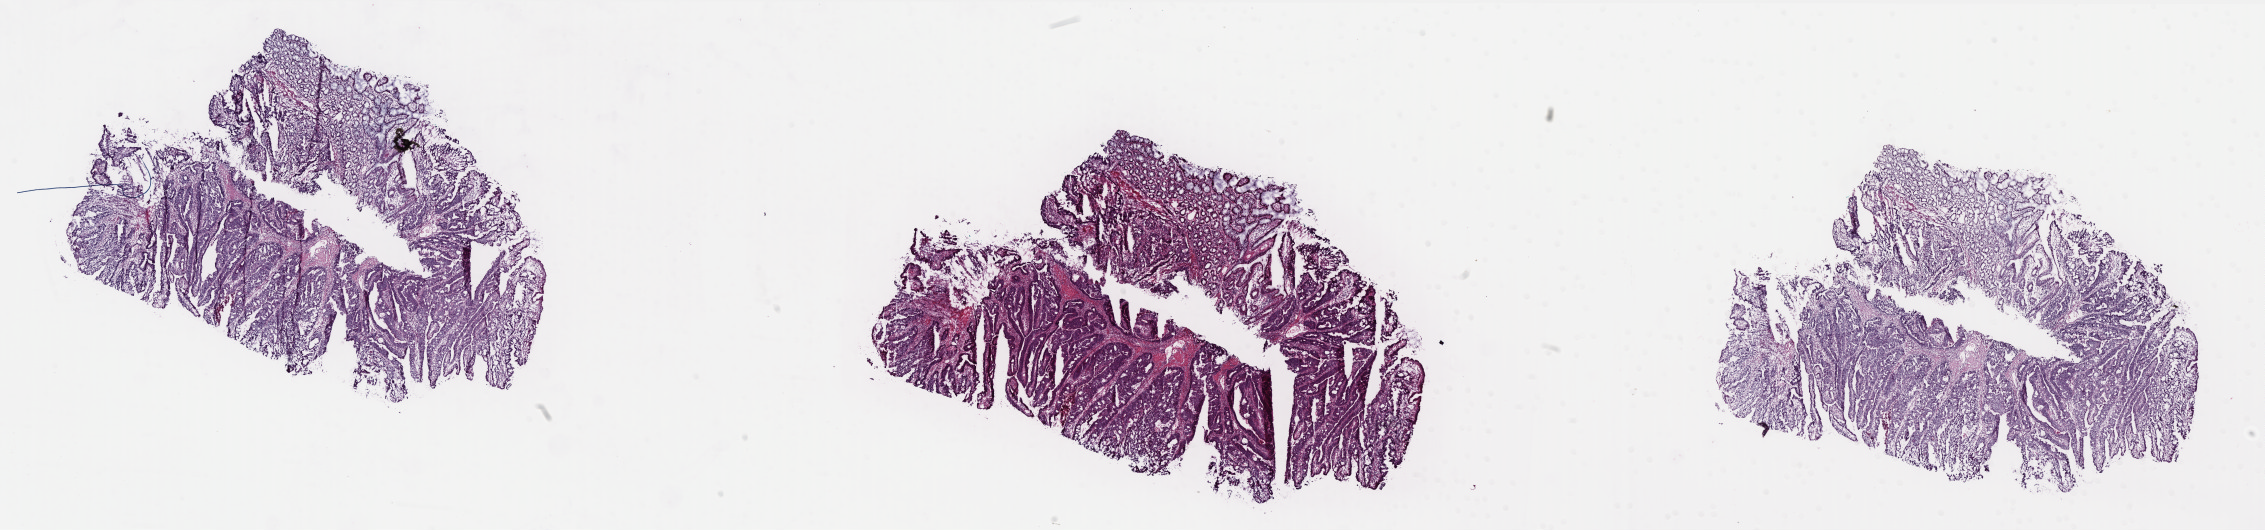
Whole-slide histology image, Hematoxylin and eosin (H&E) stained — whole scanned area (about 36.3 x 8.5 mm, from a 40x scan) shown as a low-resolution overview, frozen section from the top of the tissue portion, sample: primary tumour, rectum. Female, age 68 years at initial diagnosis. Slide review estimates, as recorded: tumour cells 80%, tumour nuclei 70%, normal cells 15%, stromal cells 3%, necrosis 2%. Inflammatory infiltration, as recorded: lymphocyte infiltration 2%, monocyte infiltration 2%, neutrophil infiltration 3%.
Lymph nodes positive (case pathology): 0 of 23 examined. Histologic diagnosis: Adenocarcinoma, NOS. AJCC pathologic stage: IV.